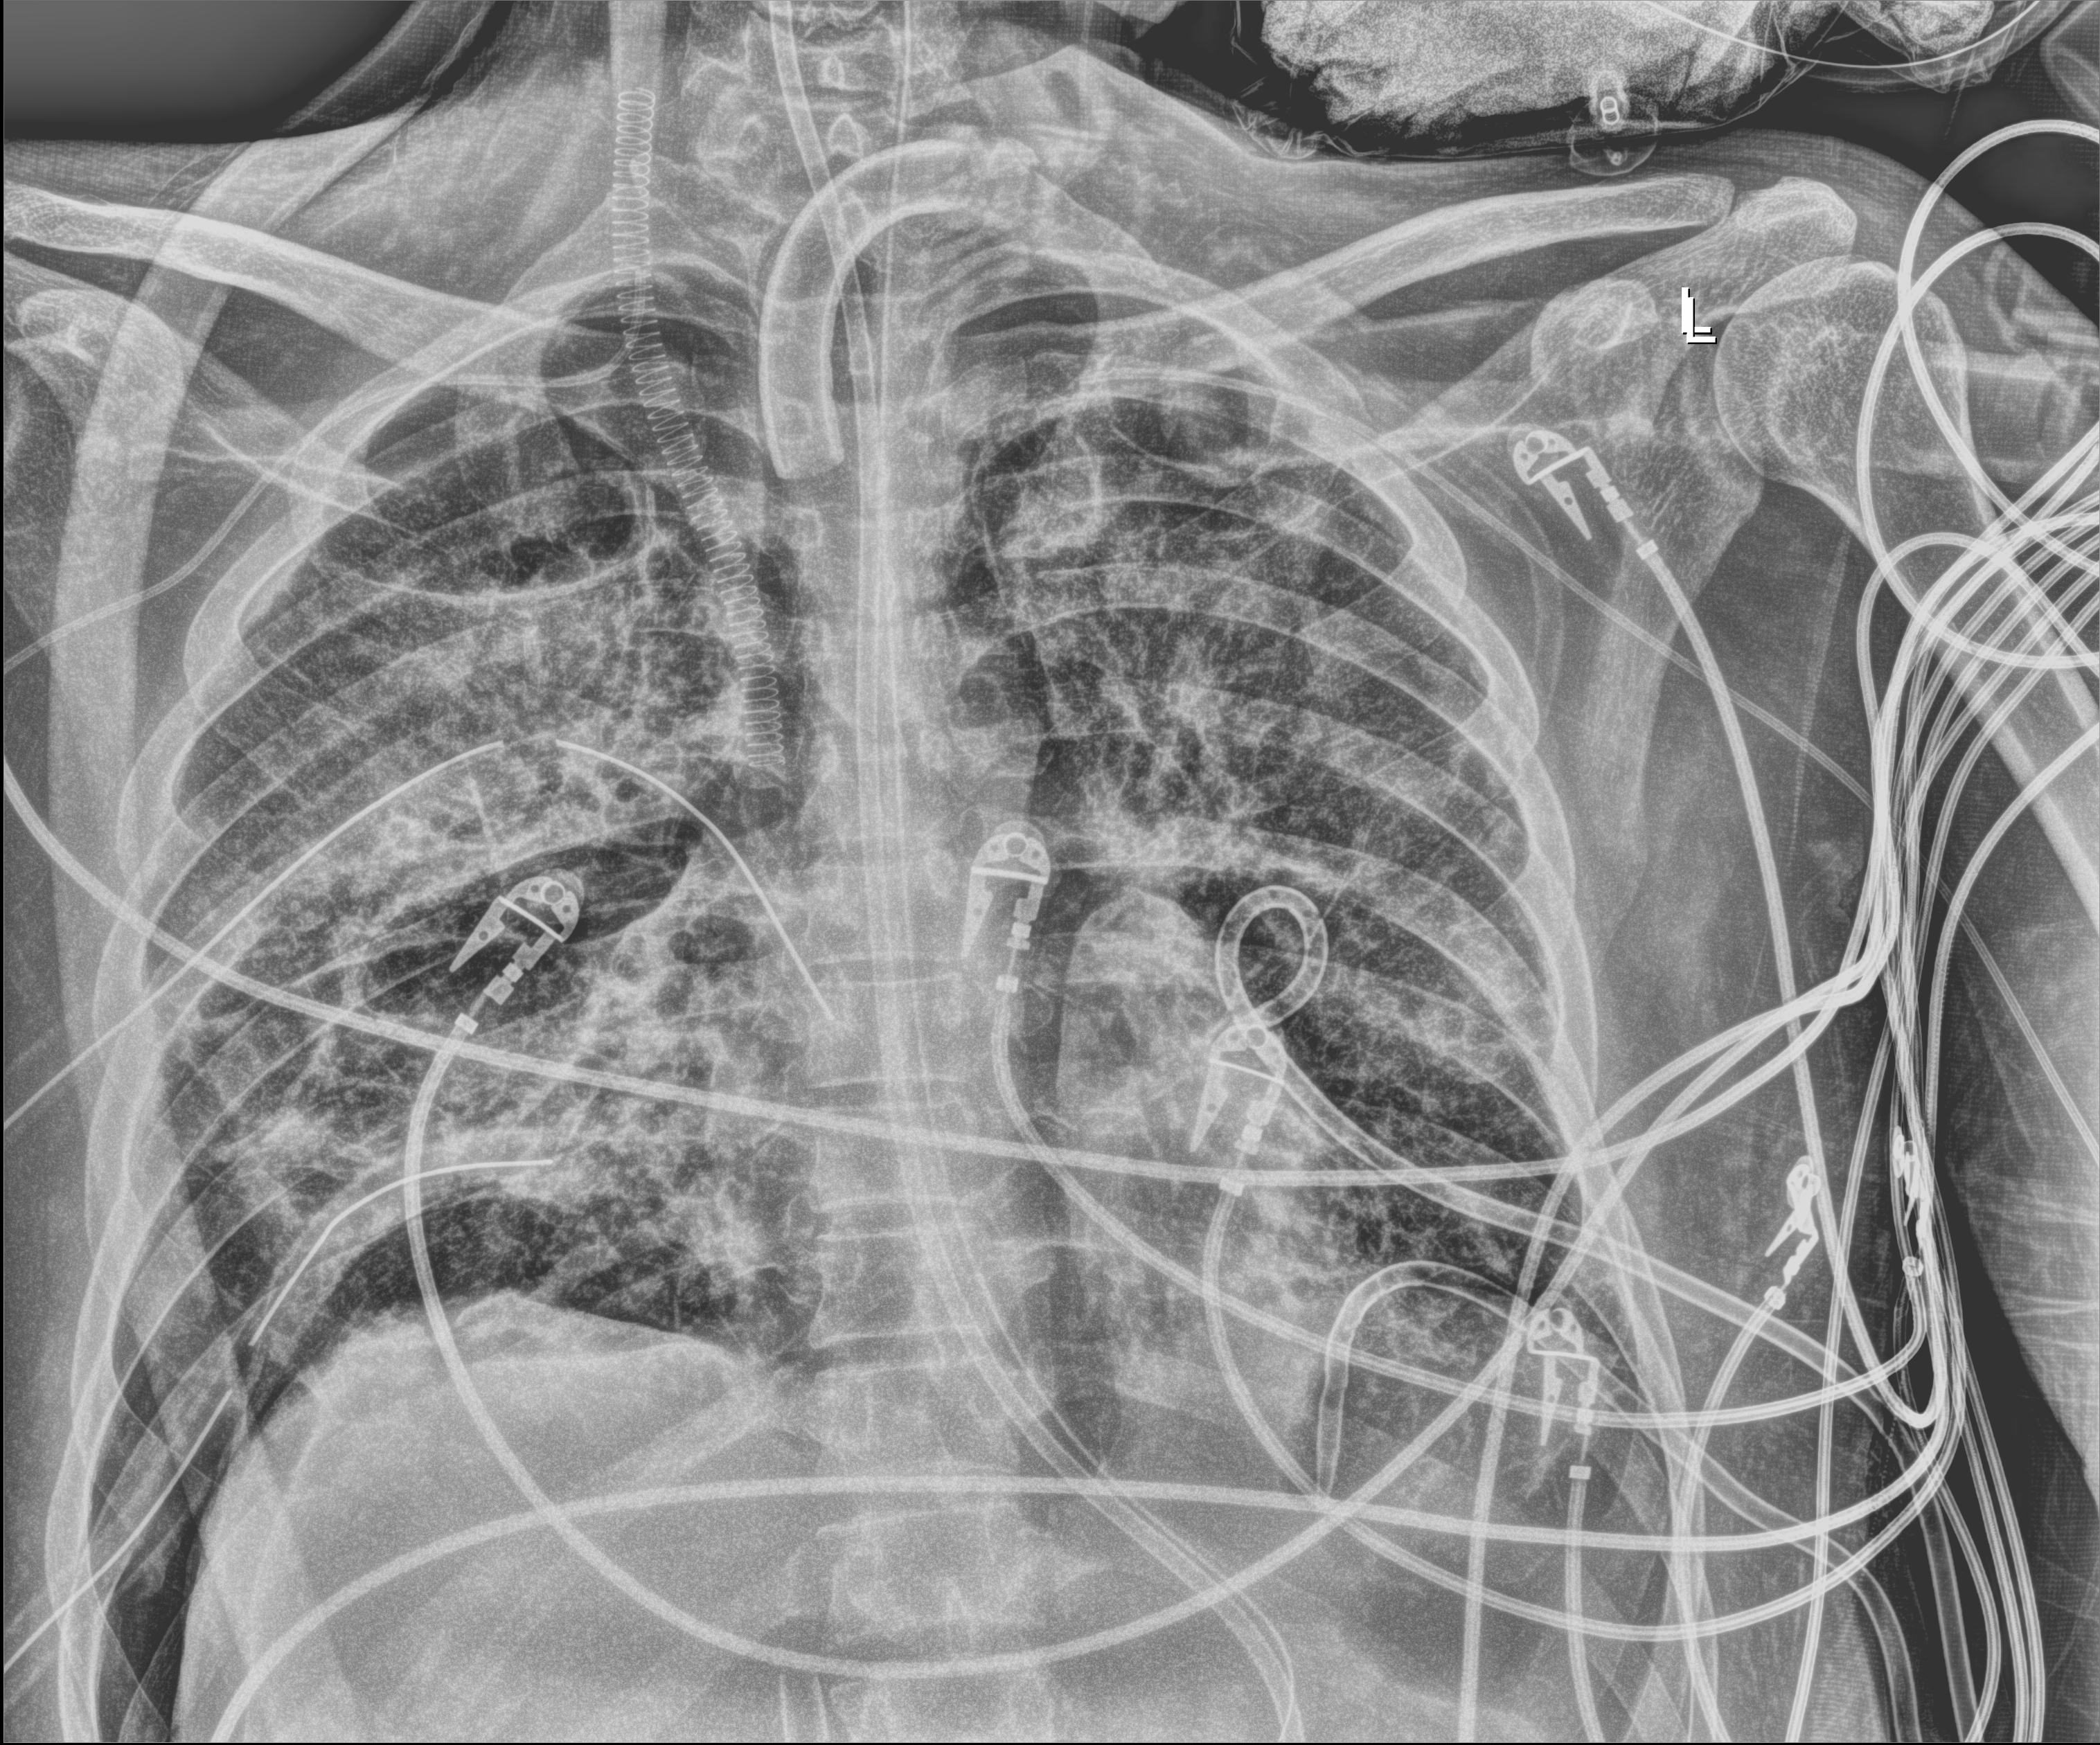
Chest X-ray (portable); anteroposterior (AP) projection. Adult patient hospitalised with COVID-19, age 18–59 years.
Admission-level facts for this patient (not findings on this image; timing relative to this image not recorded): diabetes (admission record): no.